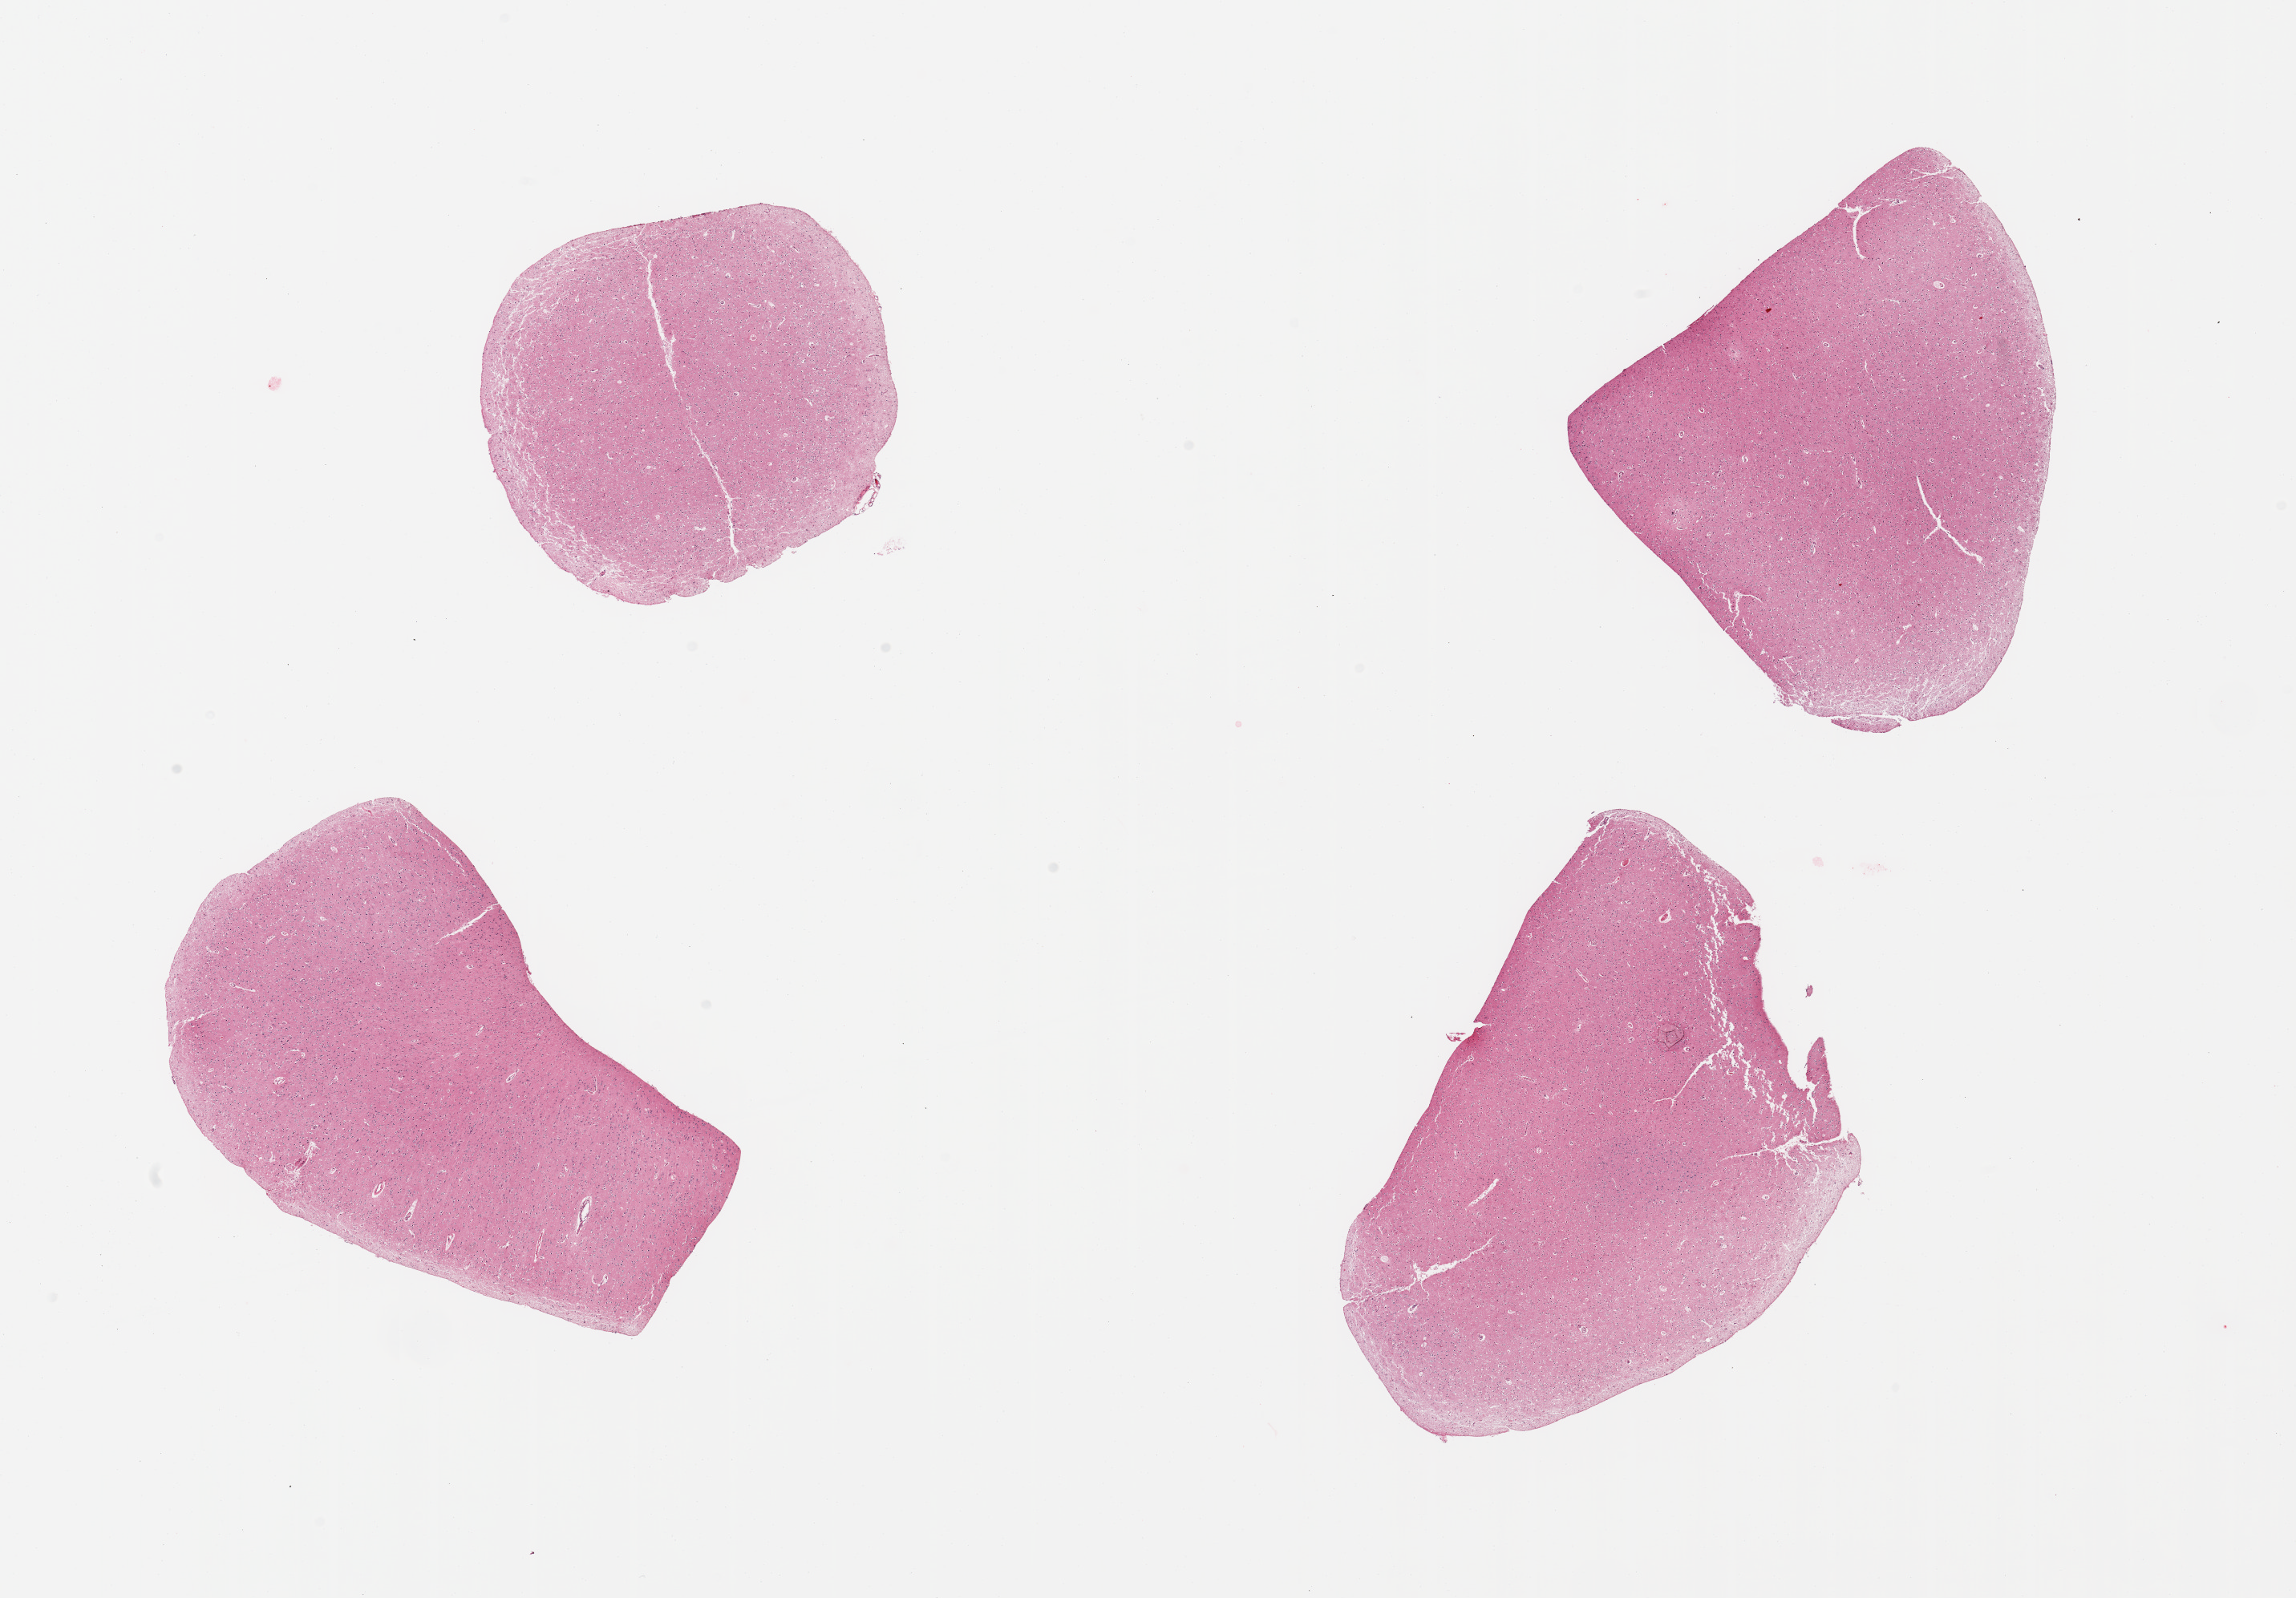
Digitized haematoxylin and eosin-stained section — a low-resolution overview of the entire scanned area, about 22.6 x 15.8 mm (from a 20x scan). PAXgene-fixed paraffin-embedded (PFPE) section. Target tissue: cerebral cortex. Donor tissue sample.
Pathologist's review note for this sample: 4 pieces, no abnormalites.